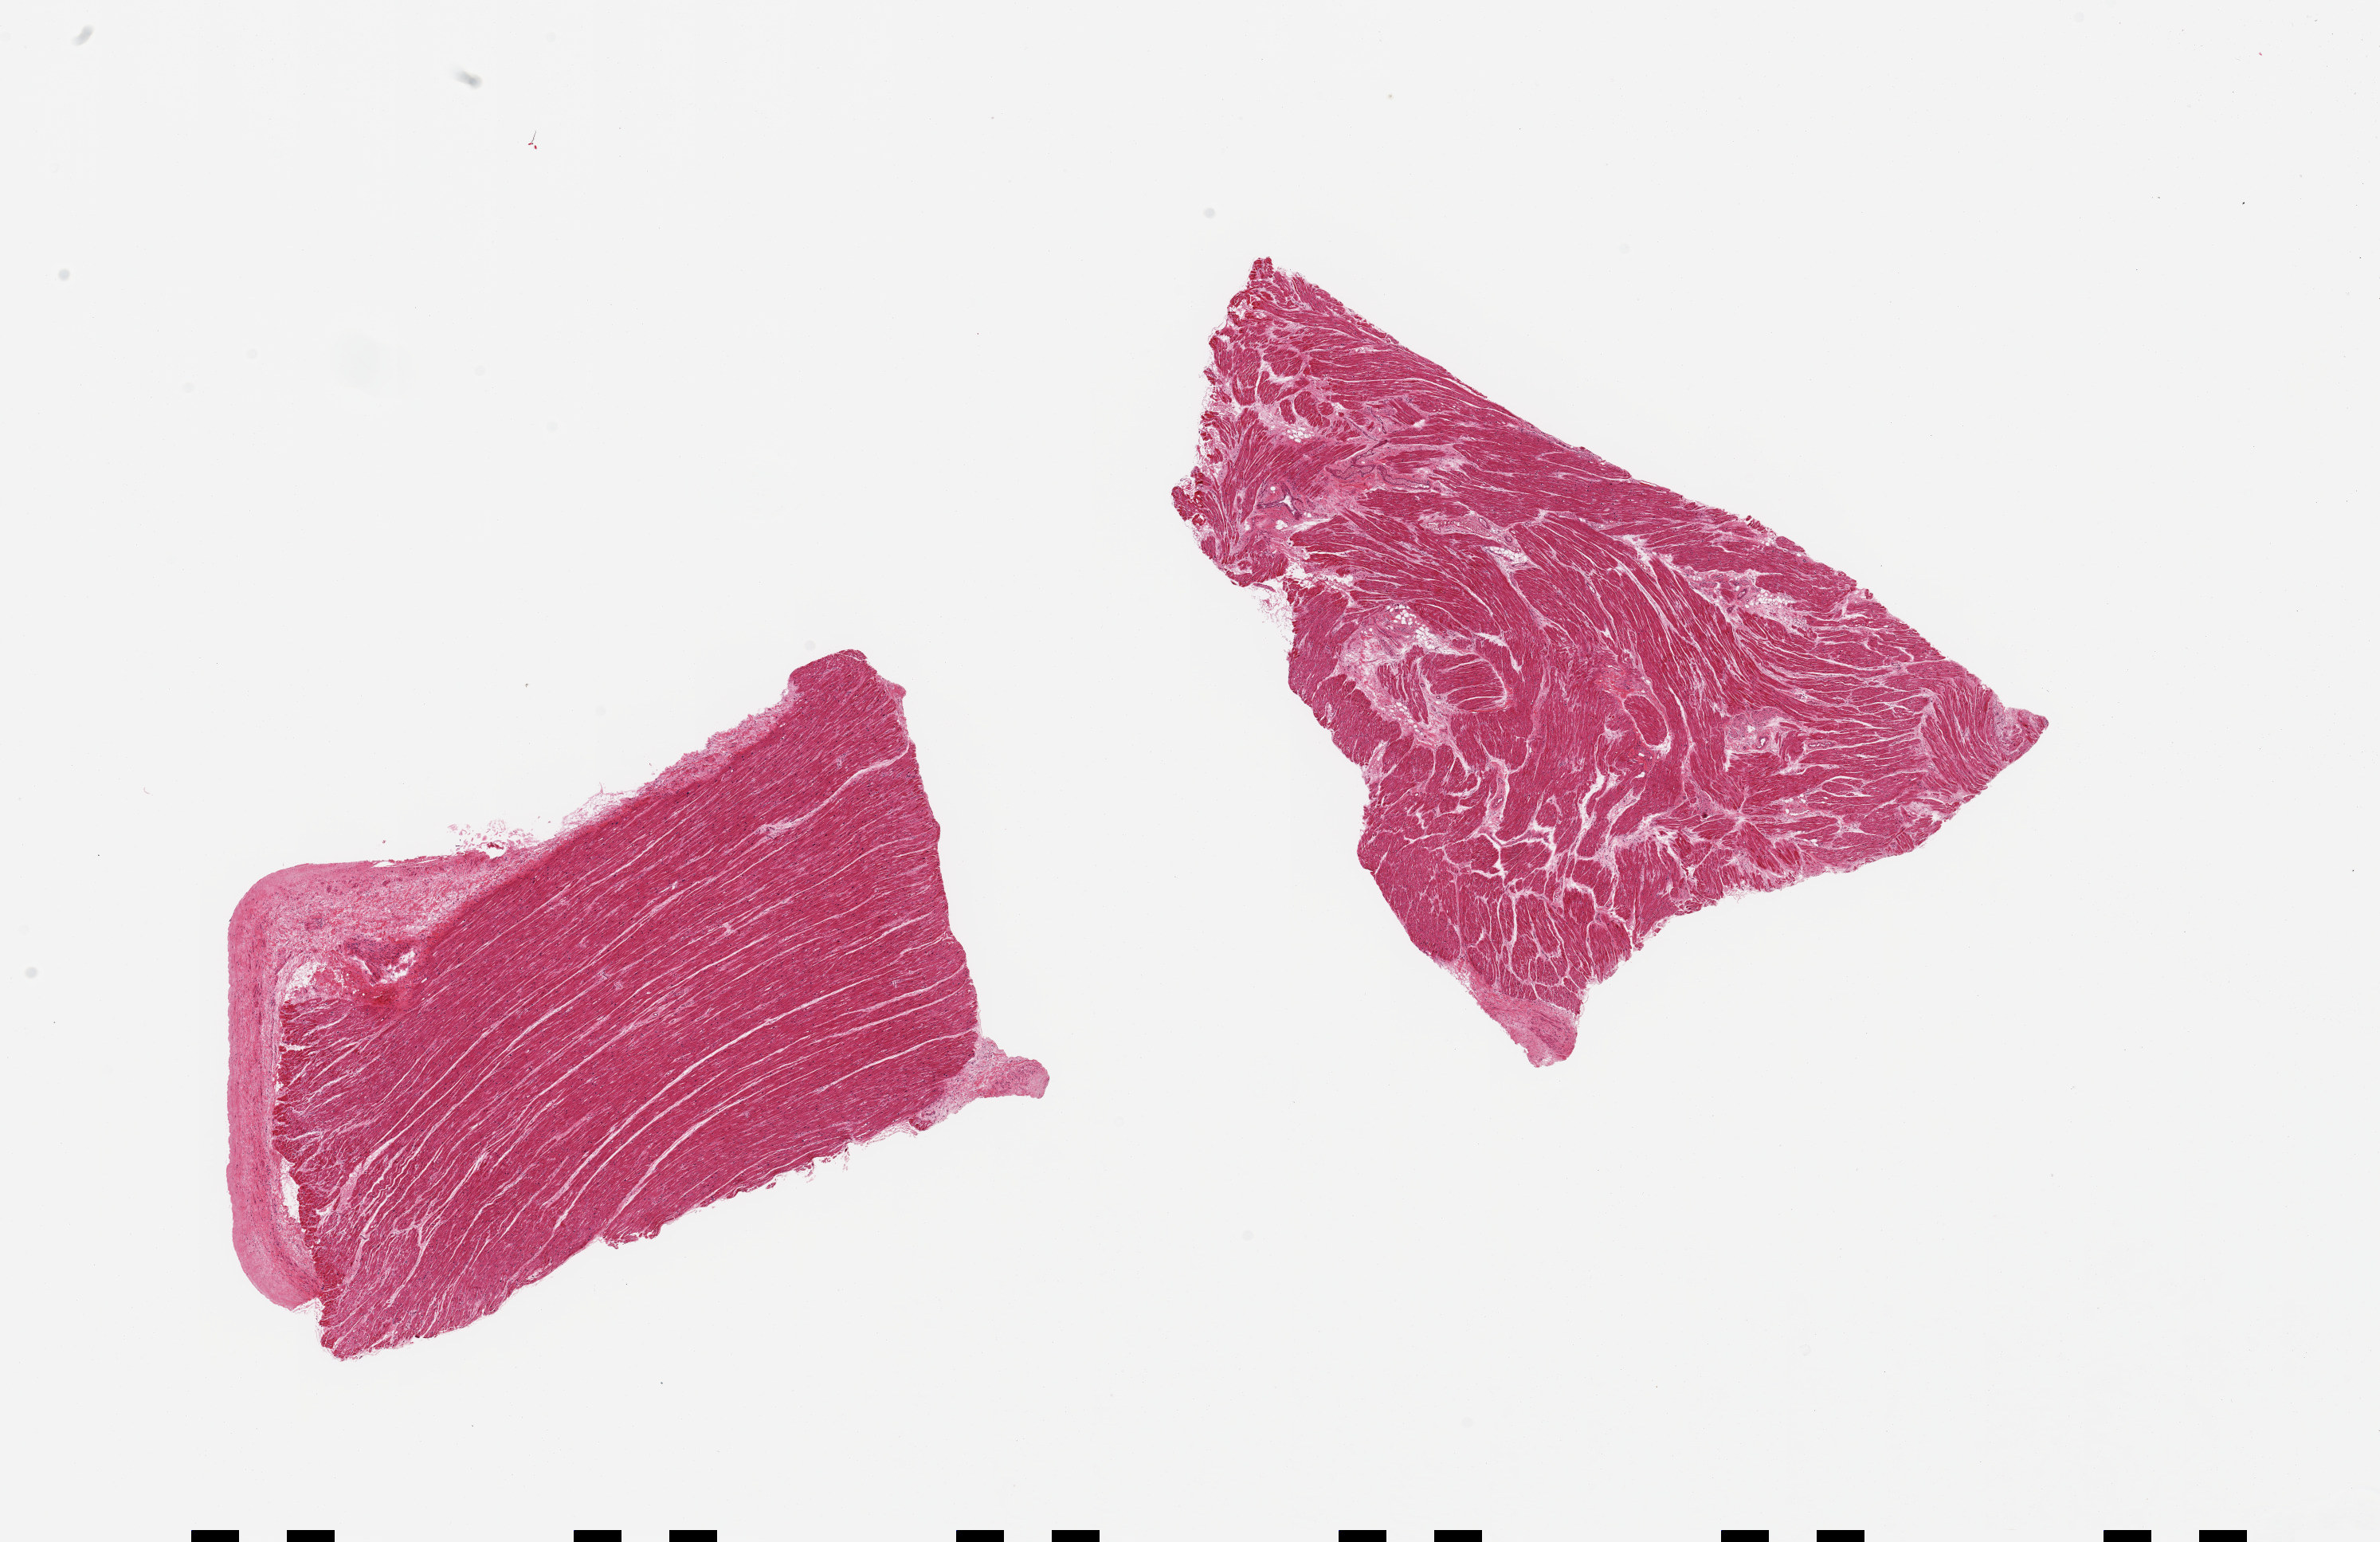
H&E whole-slide image, brightfield — shown as a low-resolution overview of the whole scanned area (about 23.6 x 15.3 mm); PAXgene-fixed, paraffin-embedded tissue; target tissue: auricular appendage; donor tissue sample. Donor: male.
Pathologist's review note for this sample: 2 pieces, no abnormality.